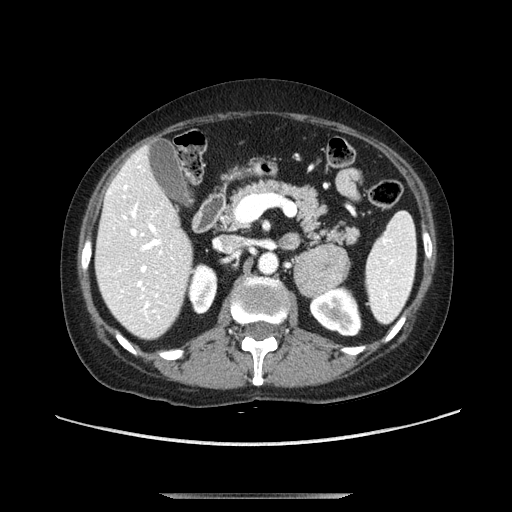
Contrast-enhanced abdominal CT, one axial slice. Slice 58 of 107 in the series (ordered by position). Soft-tissue window (W 400 / L 40 HU). 512 × 512 image matrix, field of view 380 × 380 mm. Female patient. Case-level facts recorded for this patient, not image findings: diagnosis: adrenocortical carcinoma; tumour side: left adrenal; tumour size at pathology: 7.5 cm; Ki-67 index: 9 %; stage (as recorded): 3.
Annotated regions visible in this slice (semi-automatic segmentation, software-assisted and operator-edited):
- mass: bounding box (x1, y1, x2, y2) in pixels: (295, 242, 350, 296)